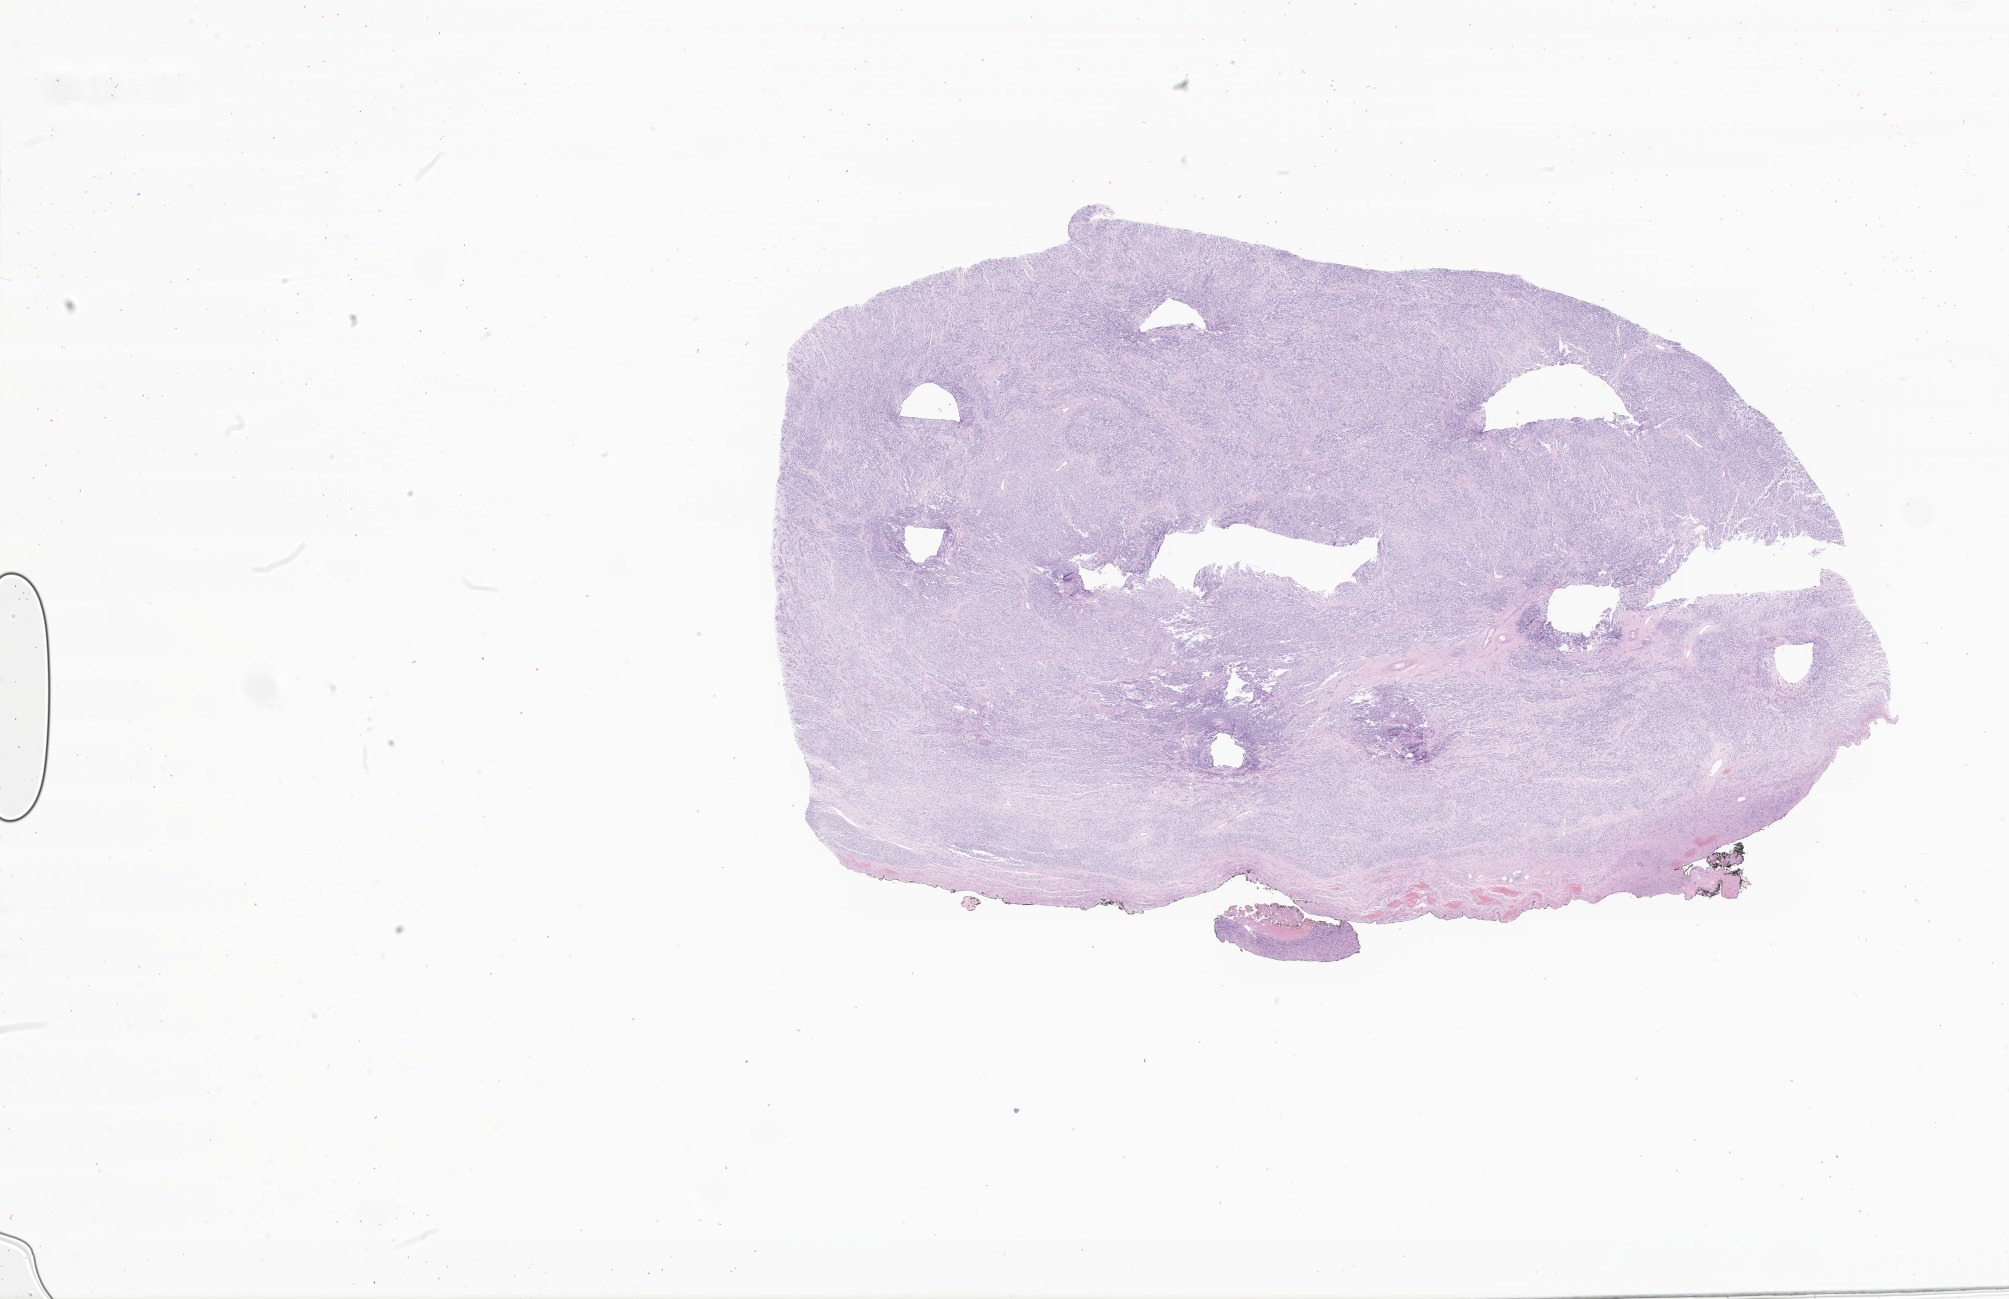
Whole-slide image, hematoxylin and eosin (H&E) stain of tumor tissue from the scrotum, shown as a low-resolution overview of the whole scanned area (about 33.9 x 21.9 mm), FFPE section. Male patient, age 183 months (15 years 3 months).
- diagnosis: Rhabdomyosarcoma, NOS